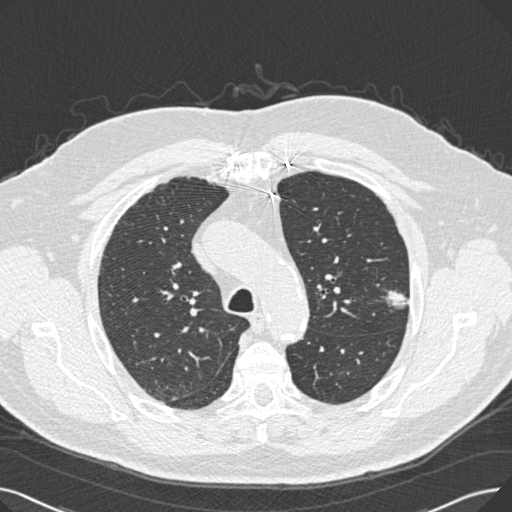
Low-dose screening chest CT, one axial slice. Slice 192 of 269 in the series (ordered by position). Reconstruction kernel B30f. Lung window (W 1500 / L -600 HU). 1 mm slice thickness. 512 × 512 image matrix, field of view 370 × 370 mm.
Annotated regions visible in this slice (outlined manually by an expert reader):
- lesion 1 (tumor, upper lobe of left lung): bounding box <383,290,410,308> (left, top, right, bottom; pixels)